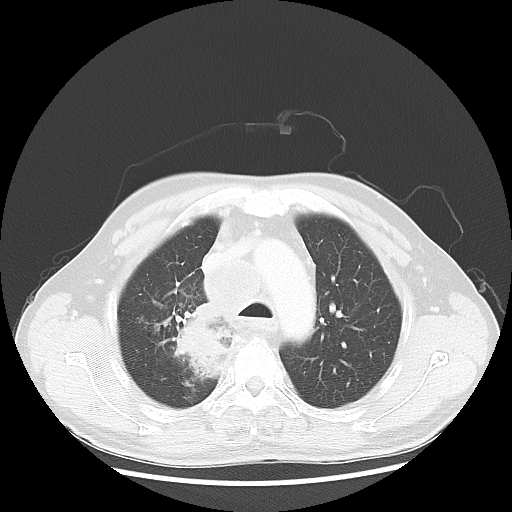
Chest CT, one axial slice. Position 43 of 60 along the scan axis. Lung window (W 1500 / L -600 HU). 512 × 512 image matrix, field of view 382 × 382 mm. Patient: male, 64 years. Case-level facts recorded for this patient, not image findings: clinical TNM (as recorded): T3 N3 M0; histopathological grade: G3.
Annotated regions visible in this slice (rectangle marked by the reading radiologist):
- lung tumour (recorded histology: small cell carcinoma): box from (x=167, y=303) to (x=245, y=389) px